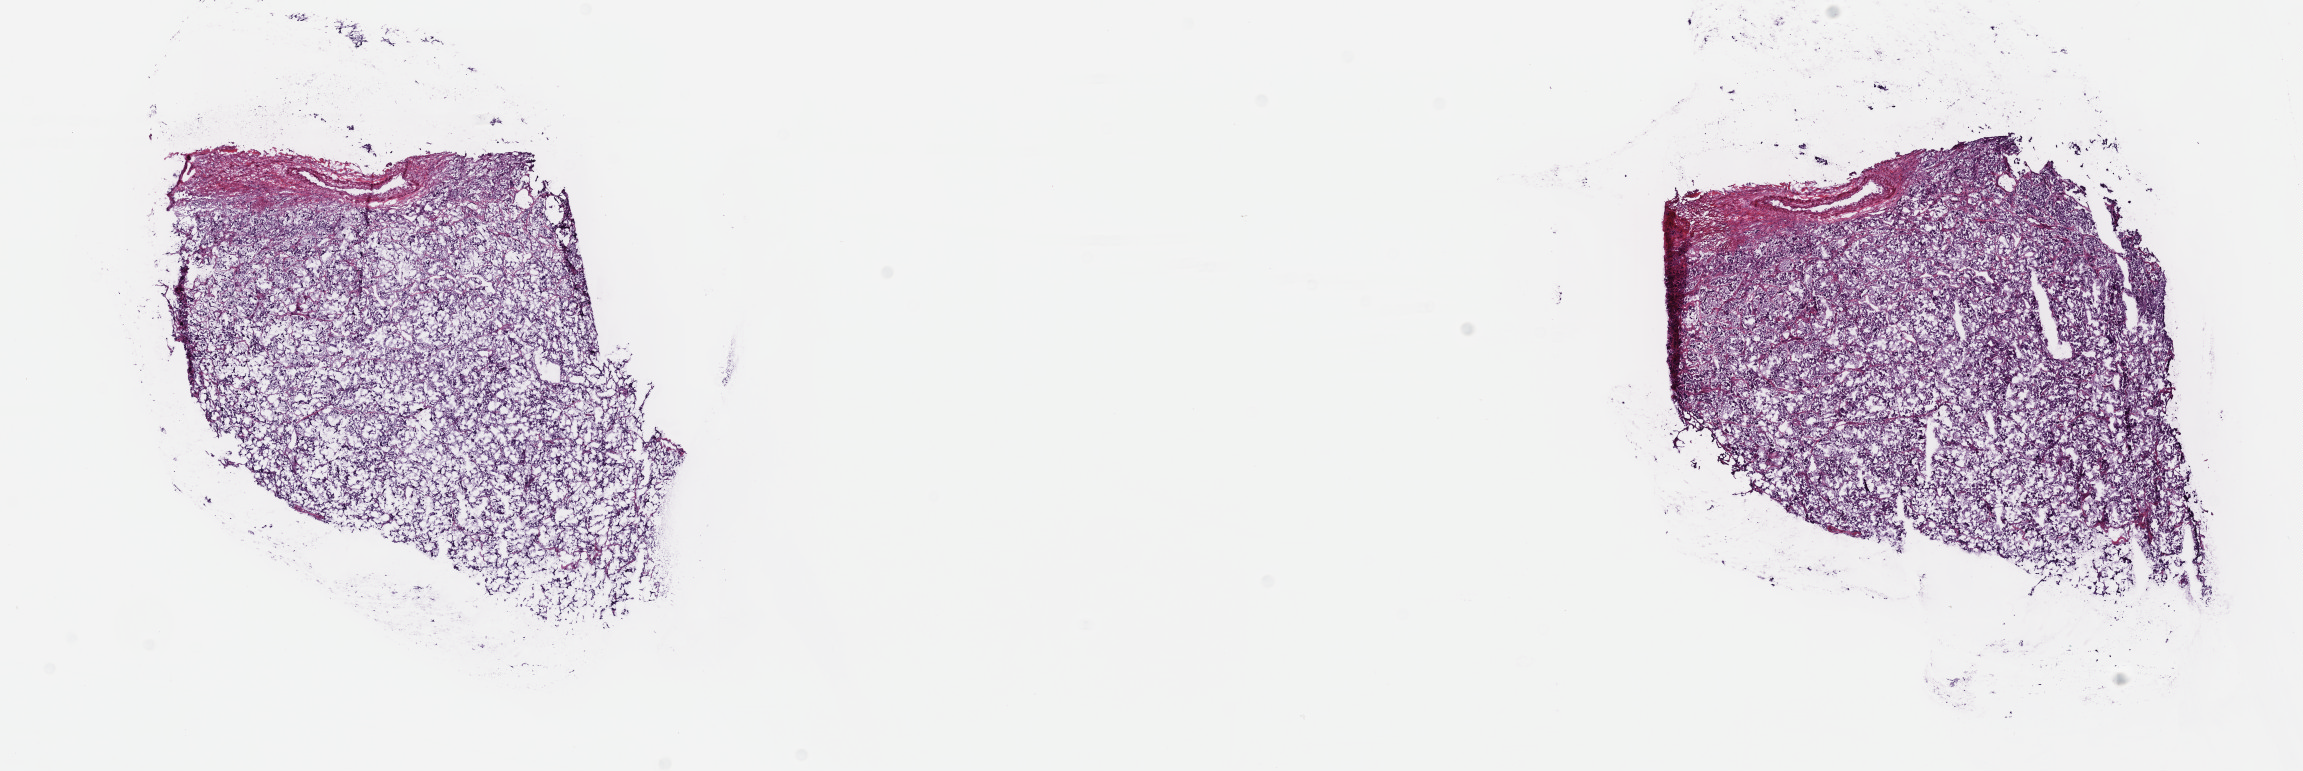
H&E-stained whole-slide image, shown as a low-resolution overview of the whole scanned area (about 18.6 x 6.2 mm), frozen section, adrenal gland, primary tumour sample. Male, age 45 years at initial diagnosis. Pathologist review of this section (percent, as recorded): tumour cells 95%, tumour nuclei 75%, normal cells 5%, stromal cells 0%, necrosis 0%. Infiltration values recorded for this section: lymphocyte infiltration 1%, monocyte infiltration 0%, neutrophil infiltration 0%.
• pathologic diagnosis: Pheochromocytoma, NOS
• laterality: left